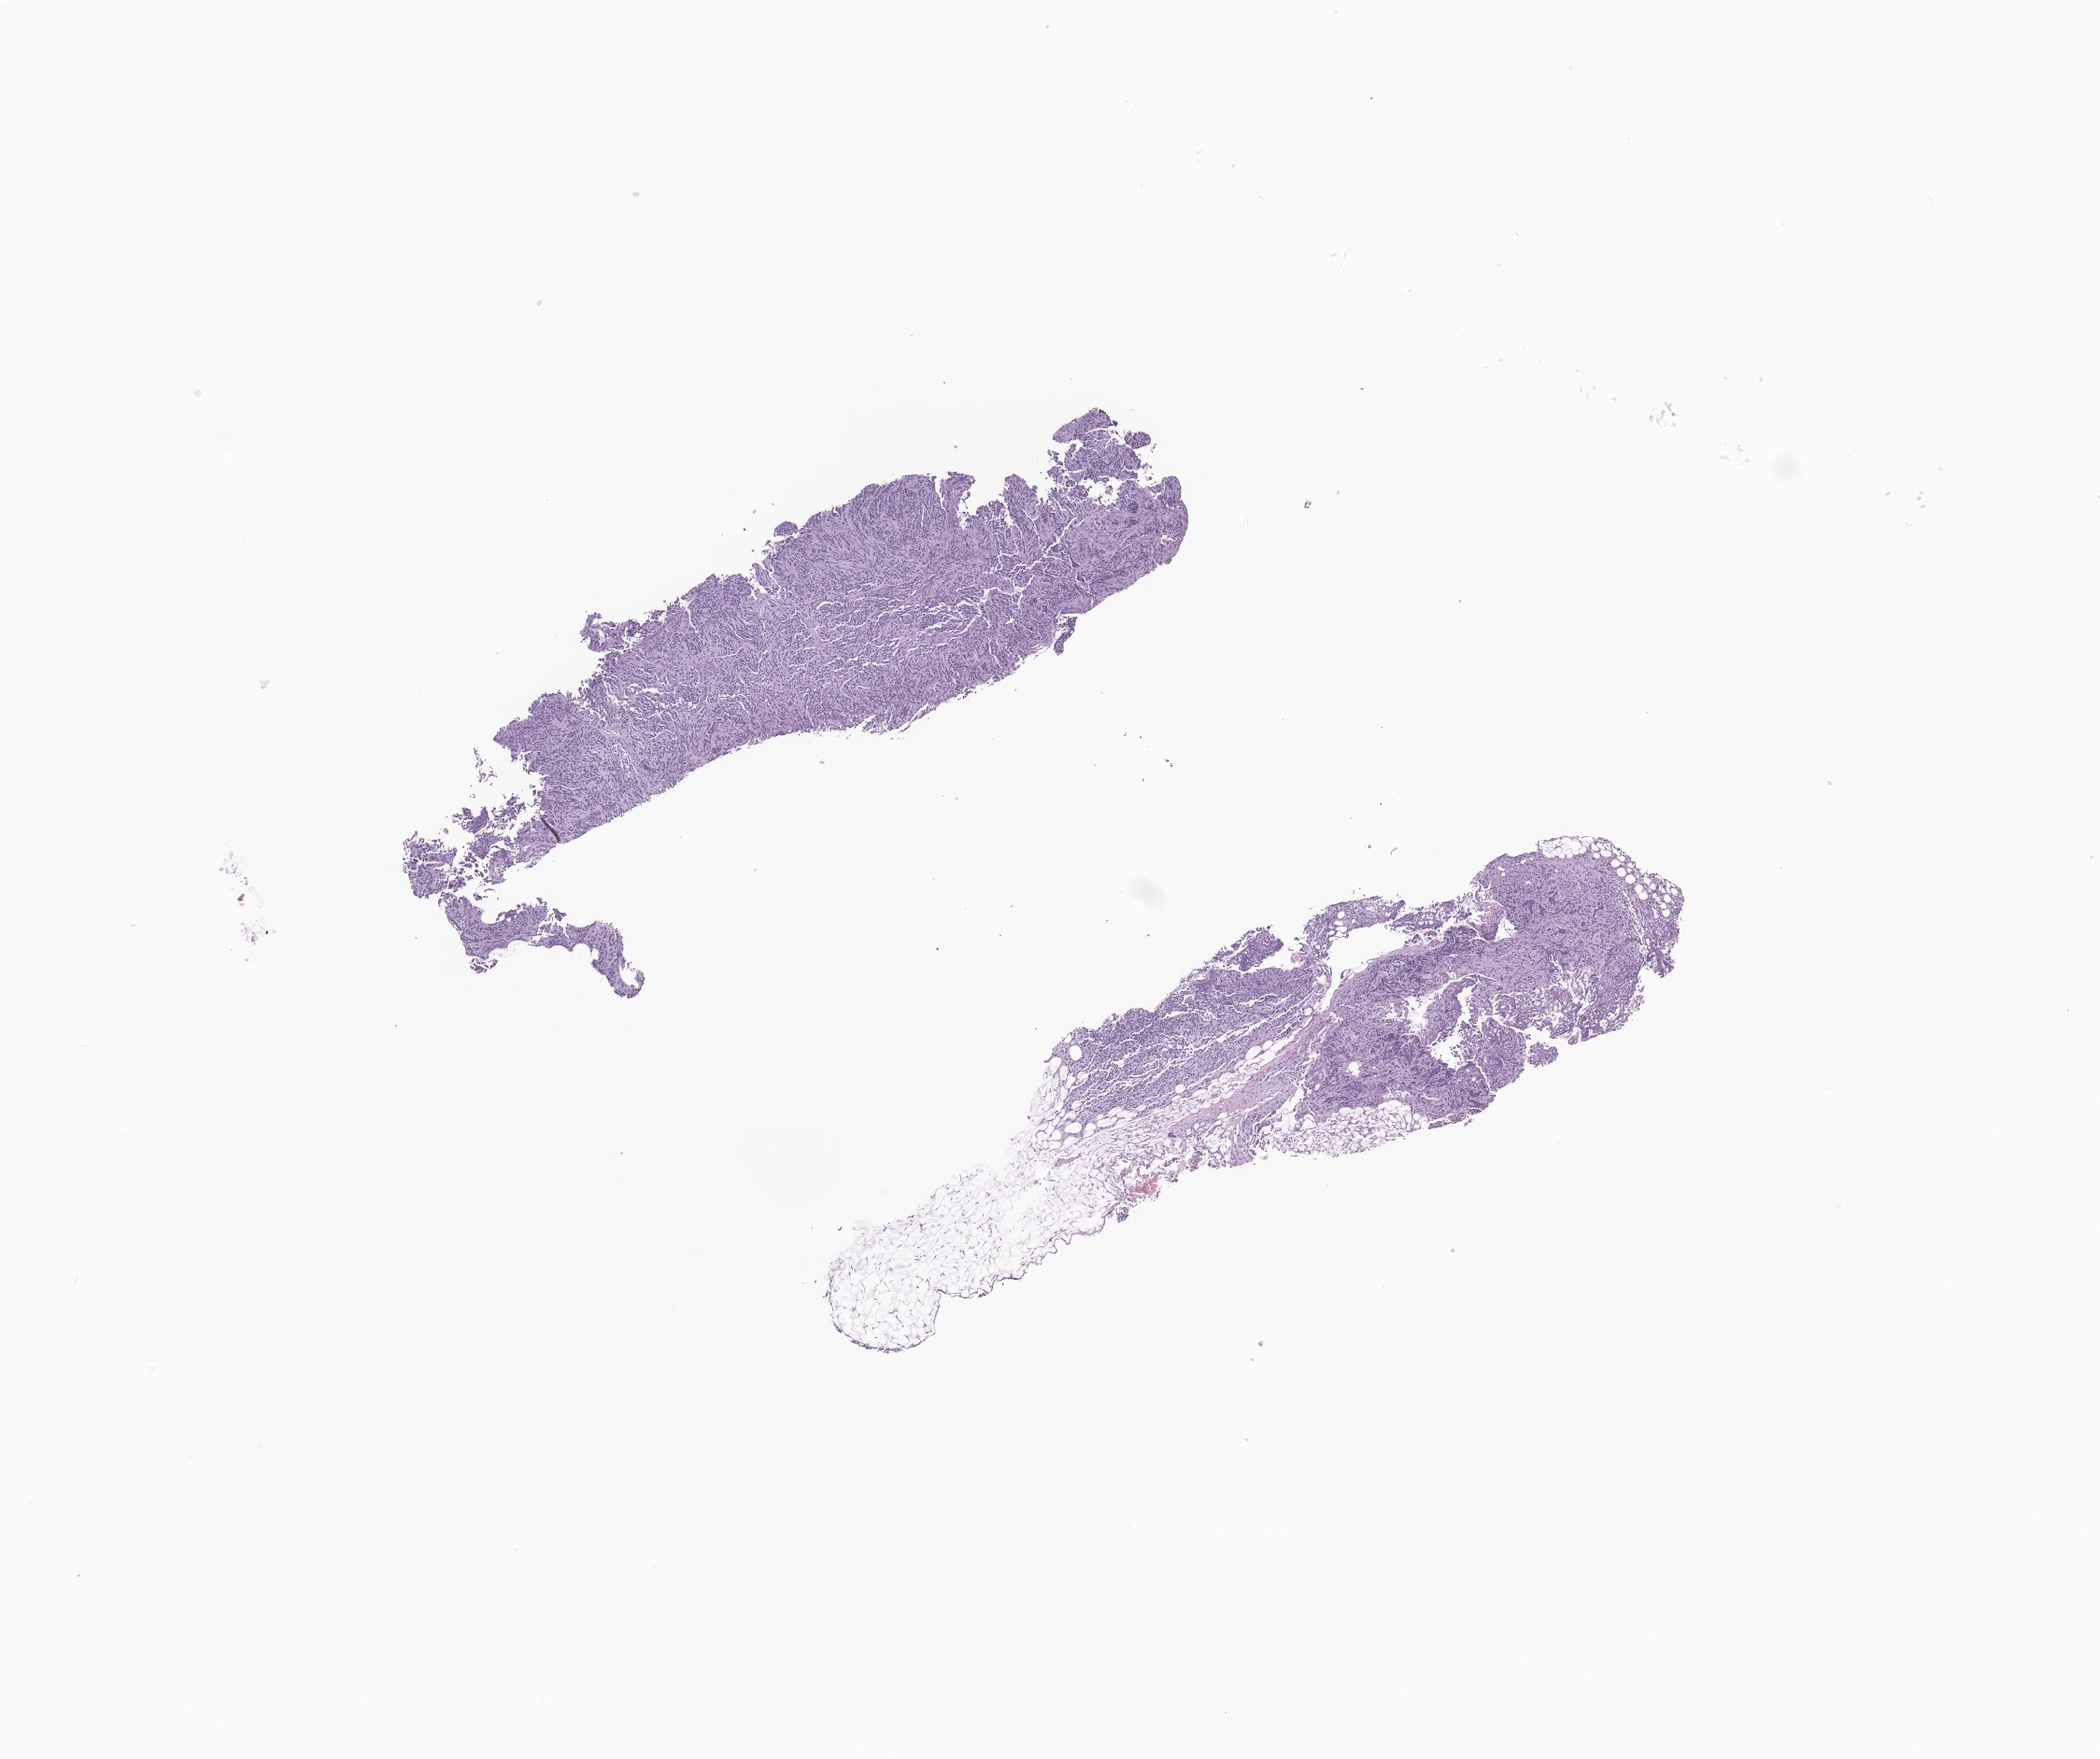
Digitized haematoxylin and eosin-stained section of tumor tissue from the posterior mediastinum — low-resolution overview of the scanned area, about 9.5 x 7.9 mm; formalin-fixed paraffin-embedded section. Patient male; age 67 days.
- diagnosis: Neuroblastoma, NOS